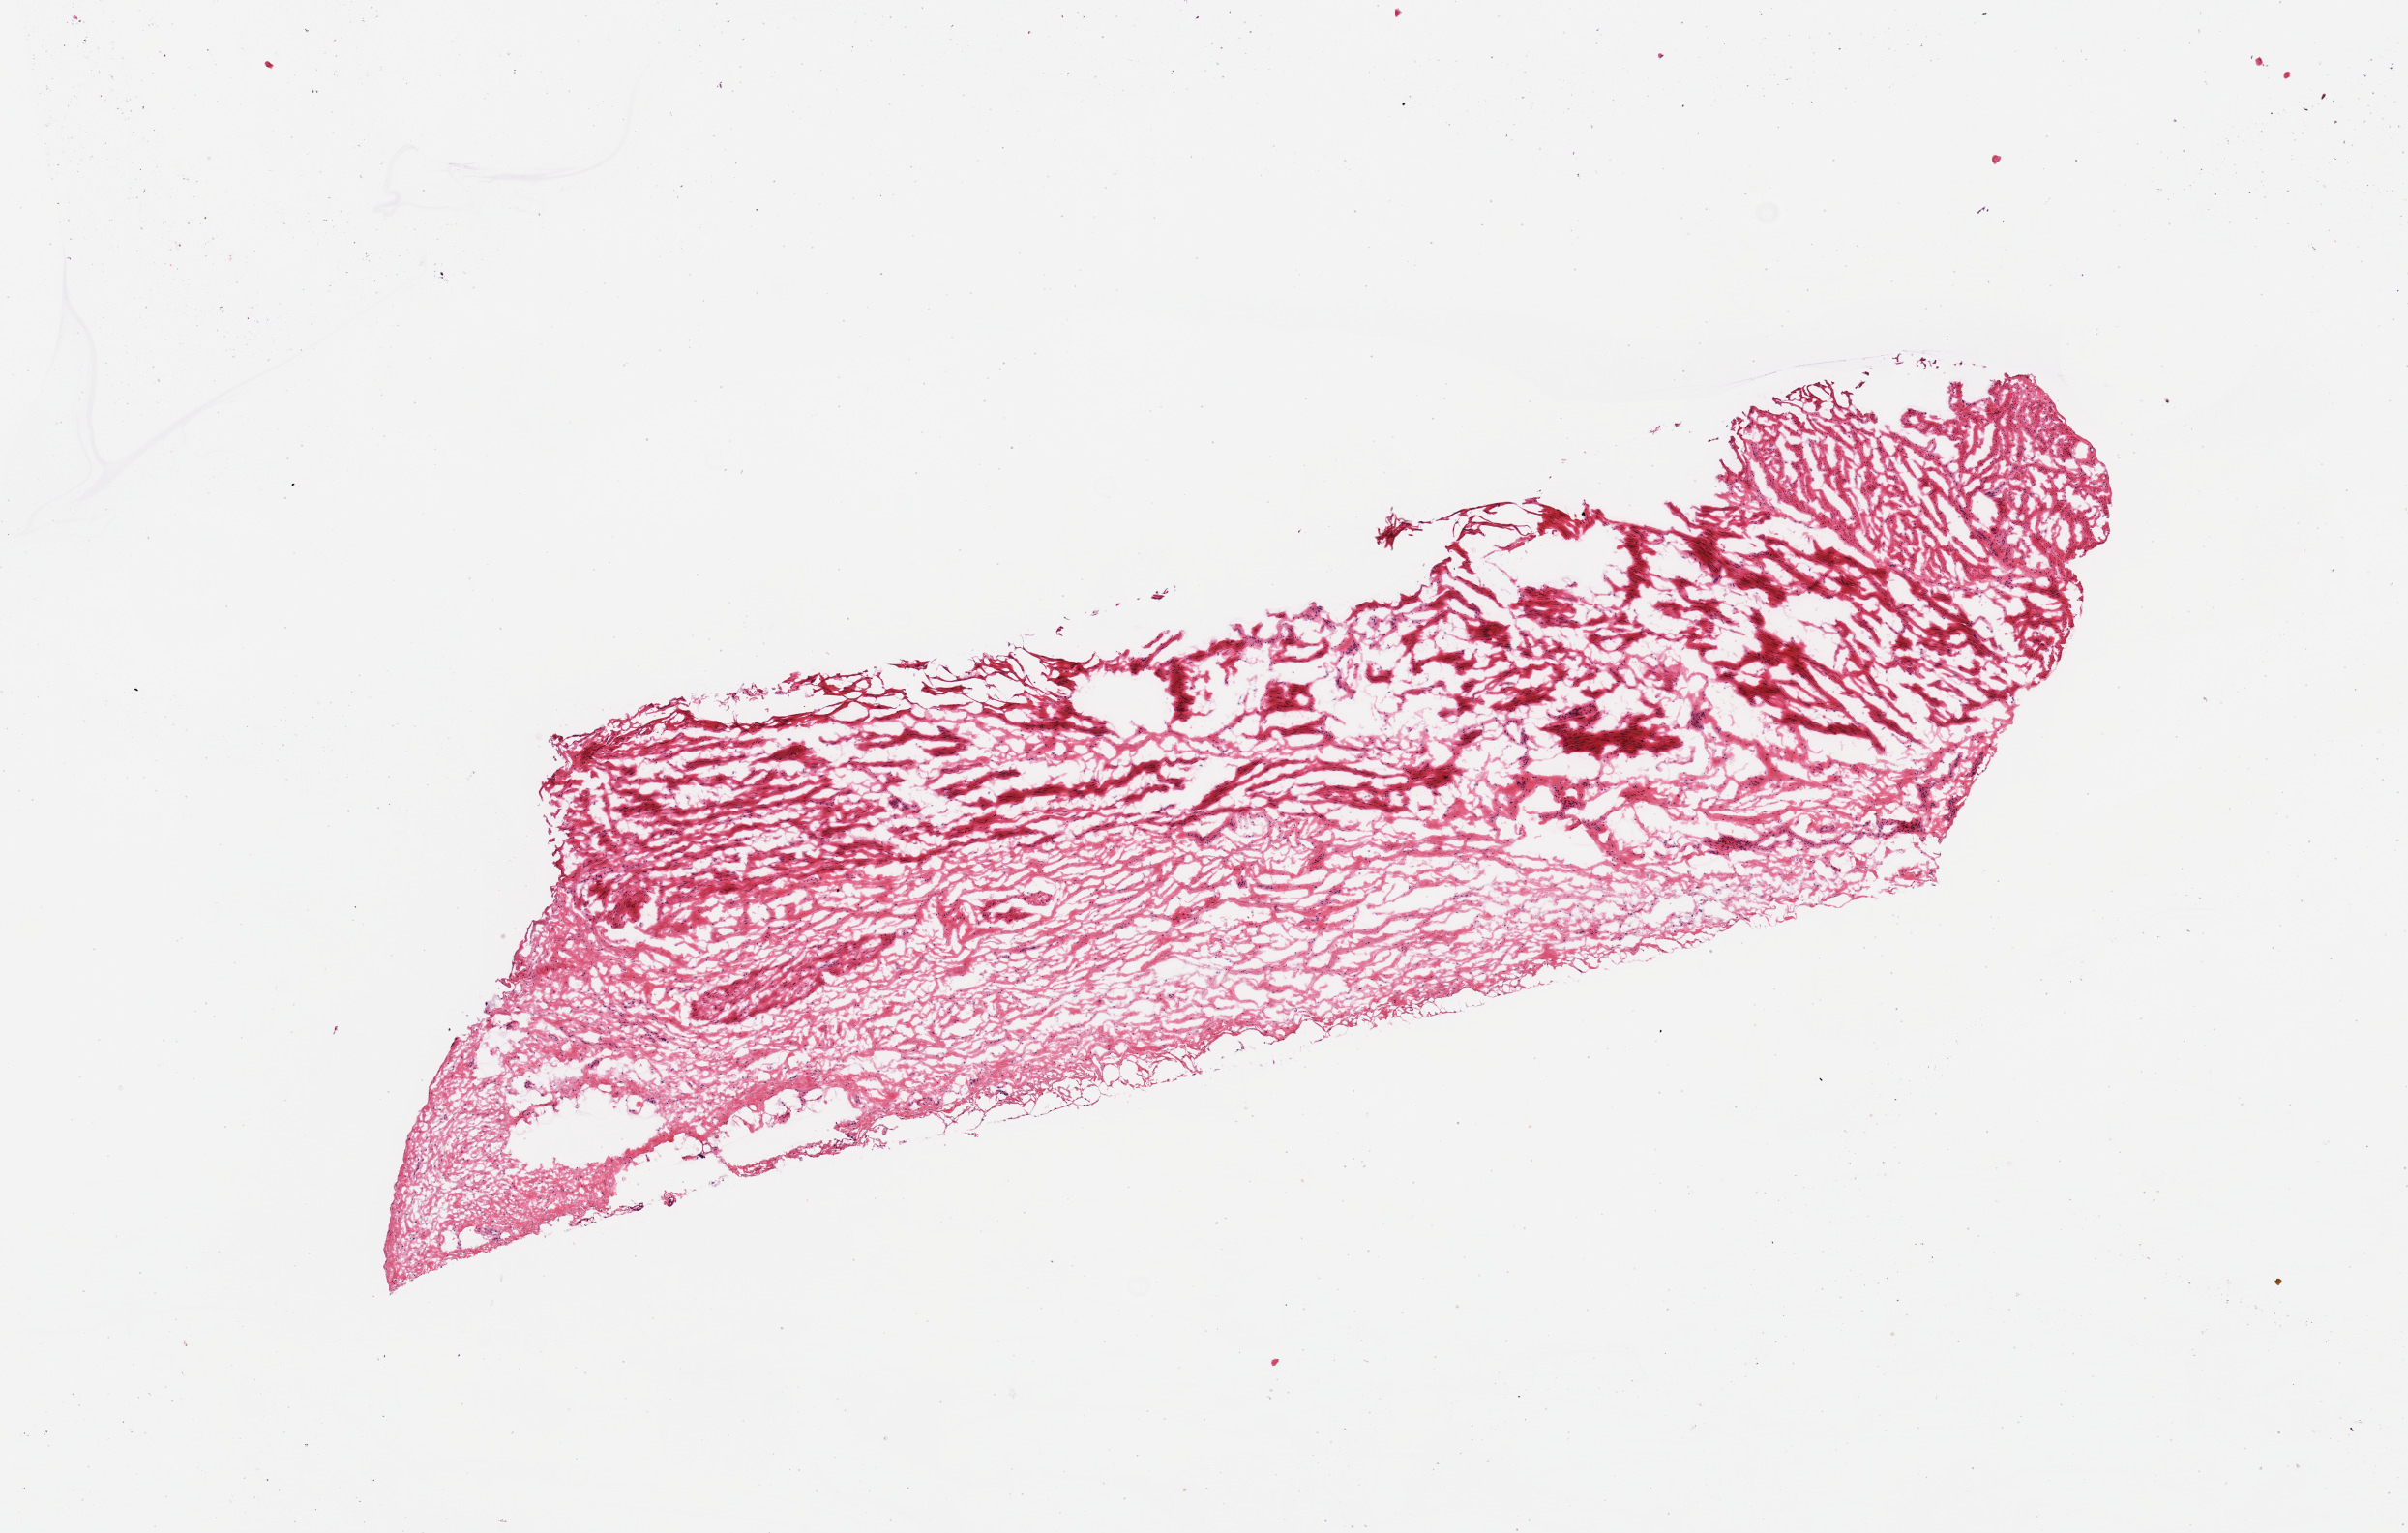
Digitized haematoxylin and eosin-stained section, shown as a low-resolution overview of the whole scanned area (about 9.8 x 6.3 mm, slide scanned at 20x). Frozen section. Target tissue: esophageal muscle. Donor tissue sample. Male donor.
Pathologist's review note for this sample: 1 piece.